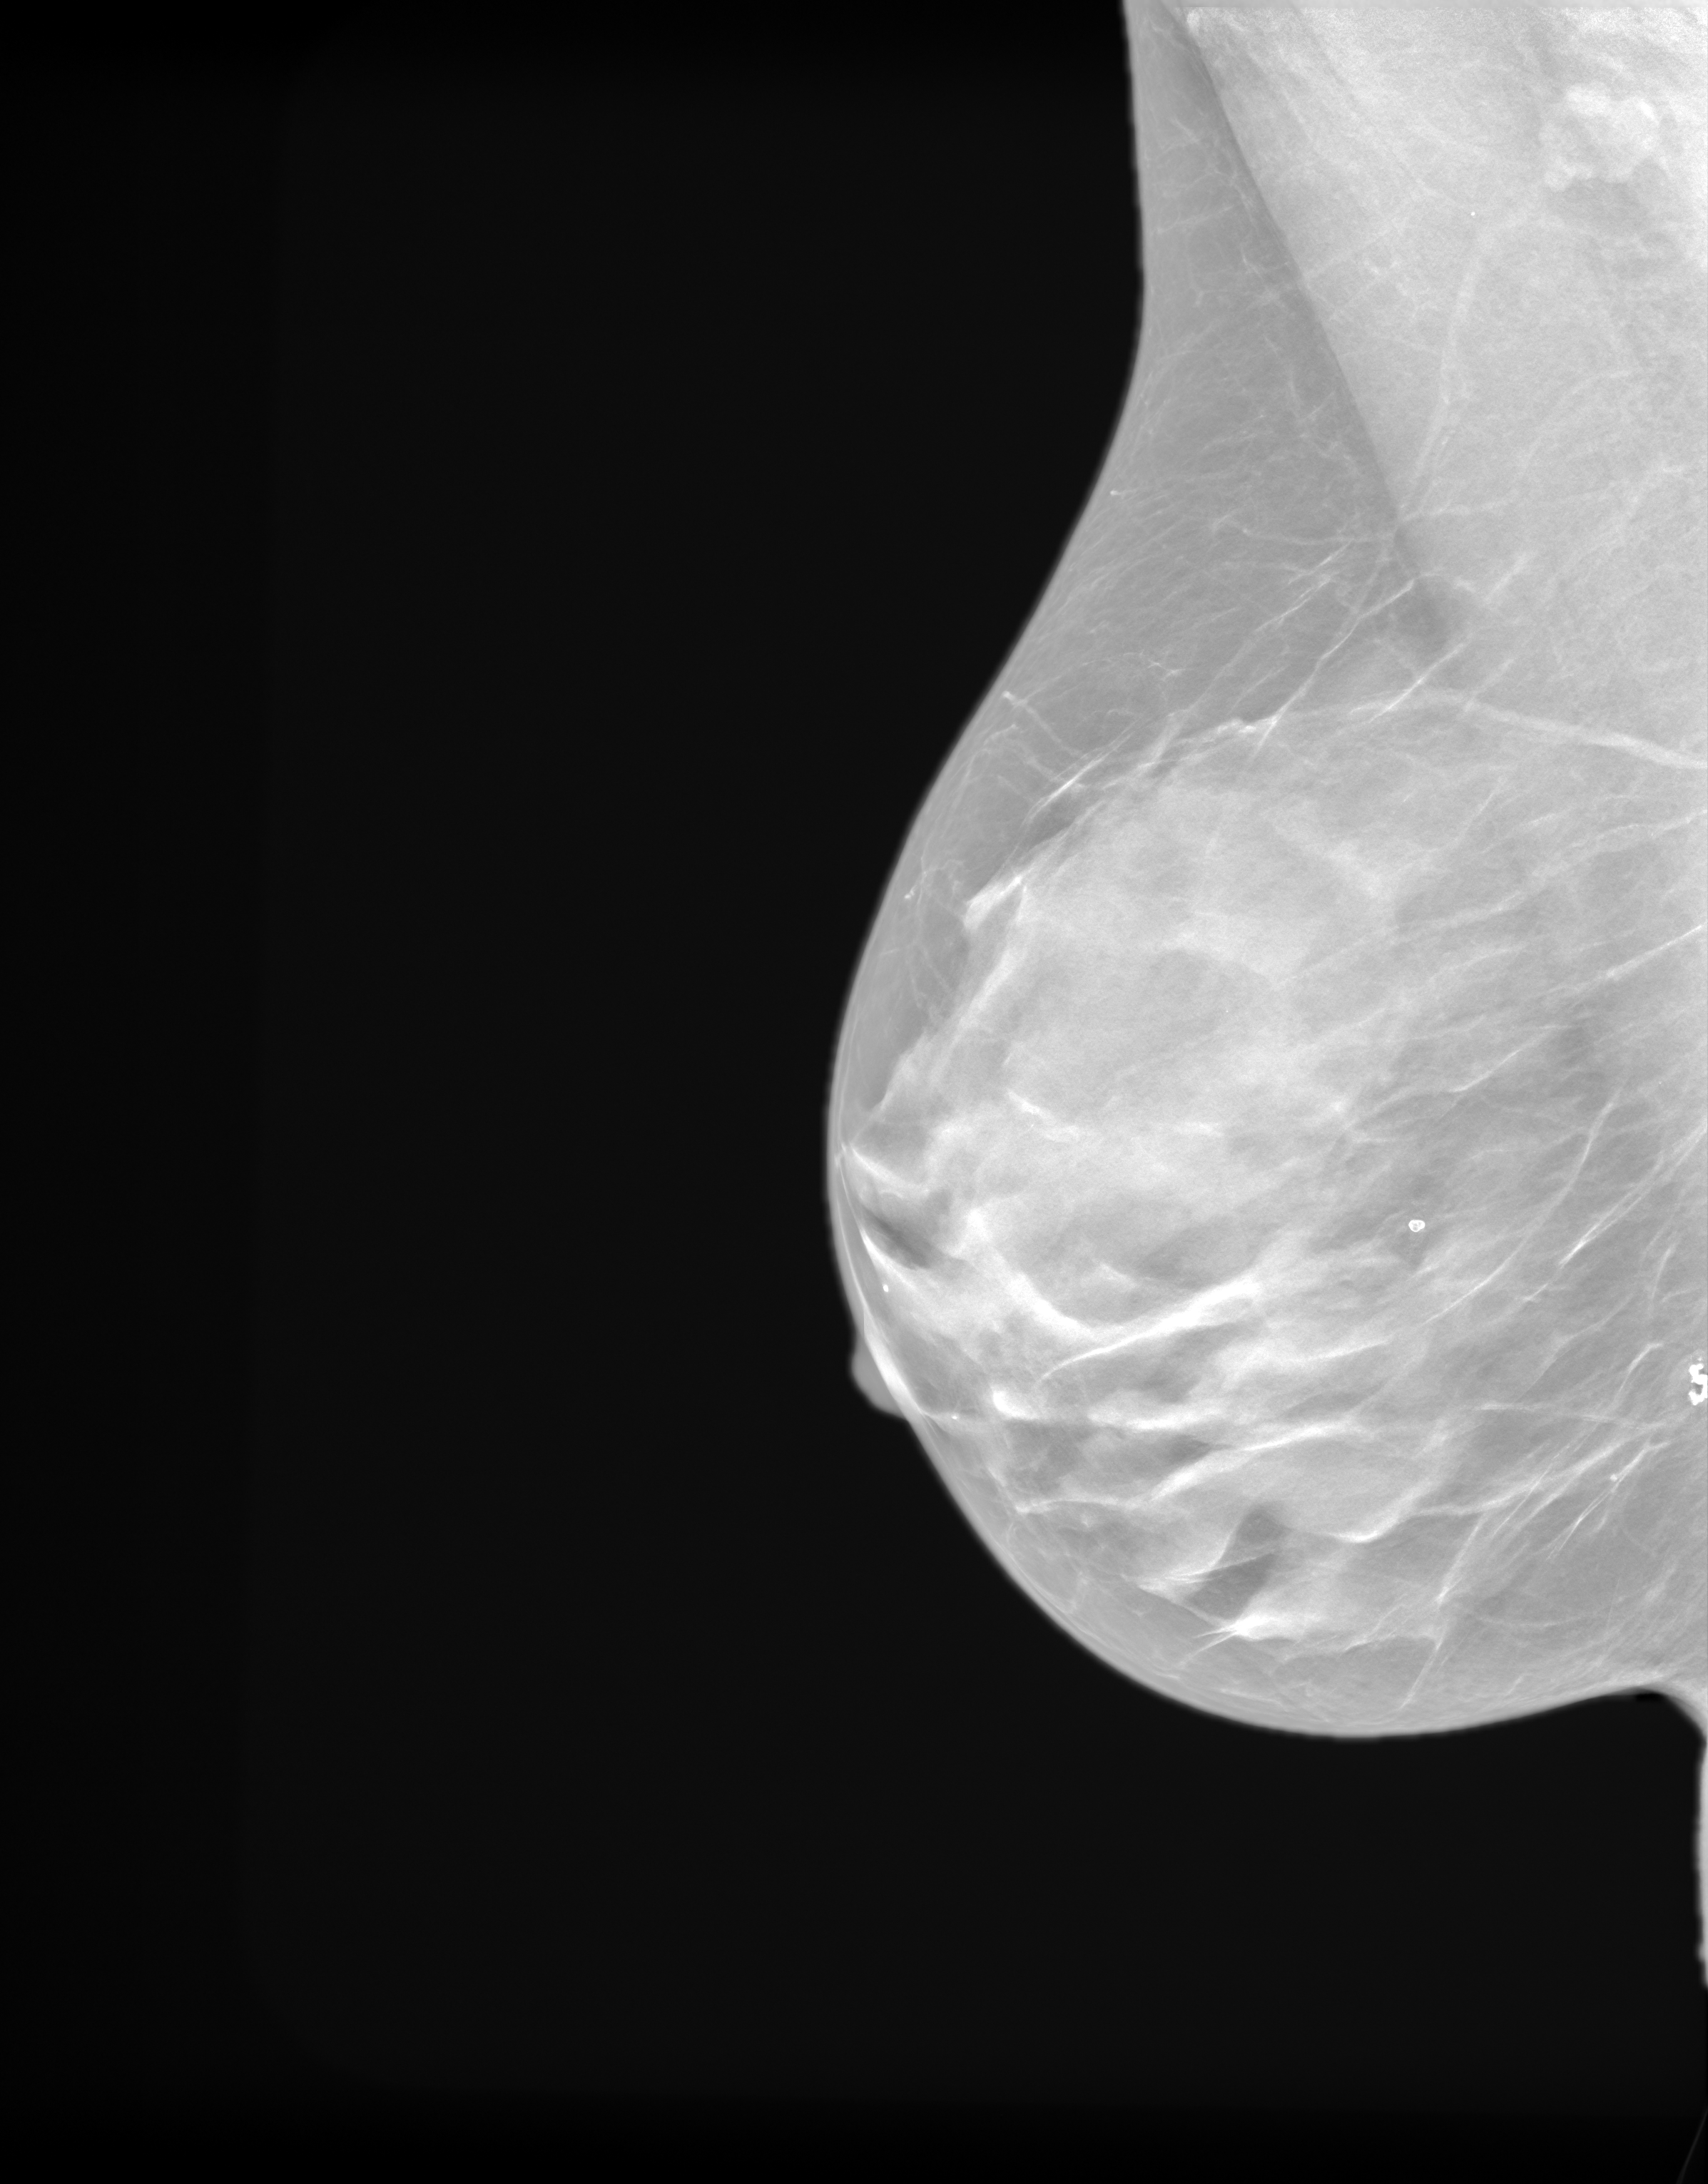
Screening examination; system: SenoIris_1SP2(440). Female patient, age 61 years.
Image type: synthesized 2-D view from tomosynthesis. Breast: right. Projection: mediolateral oblique (MLO) view.